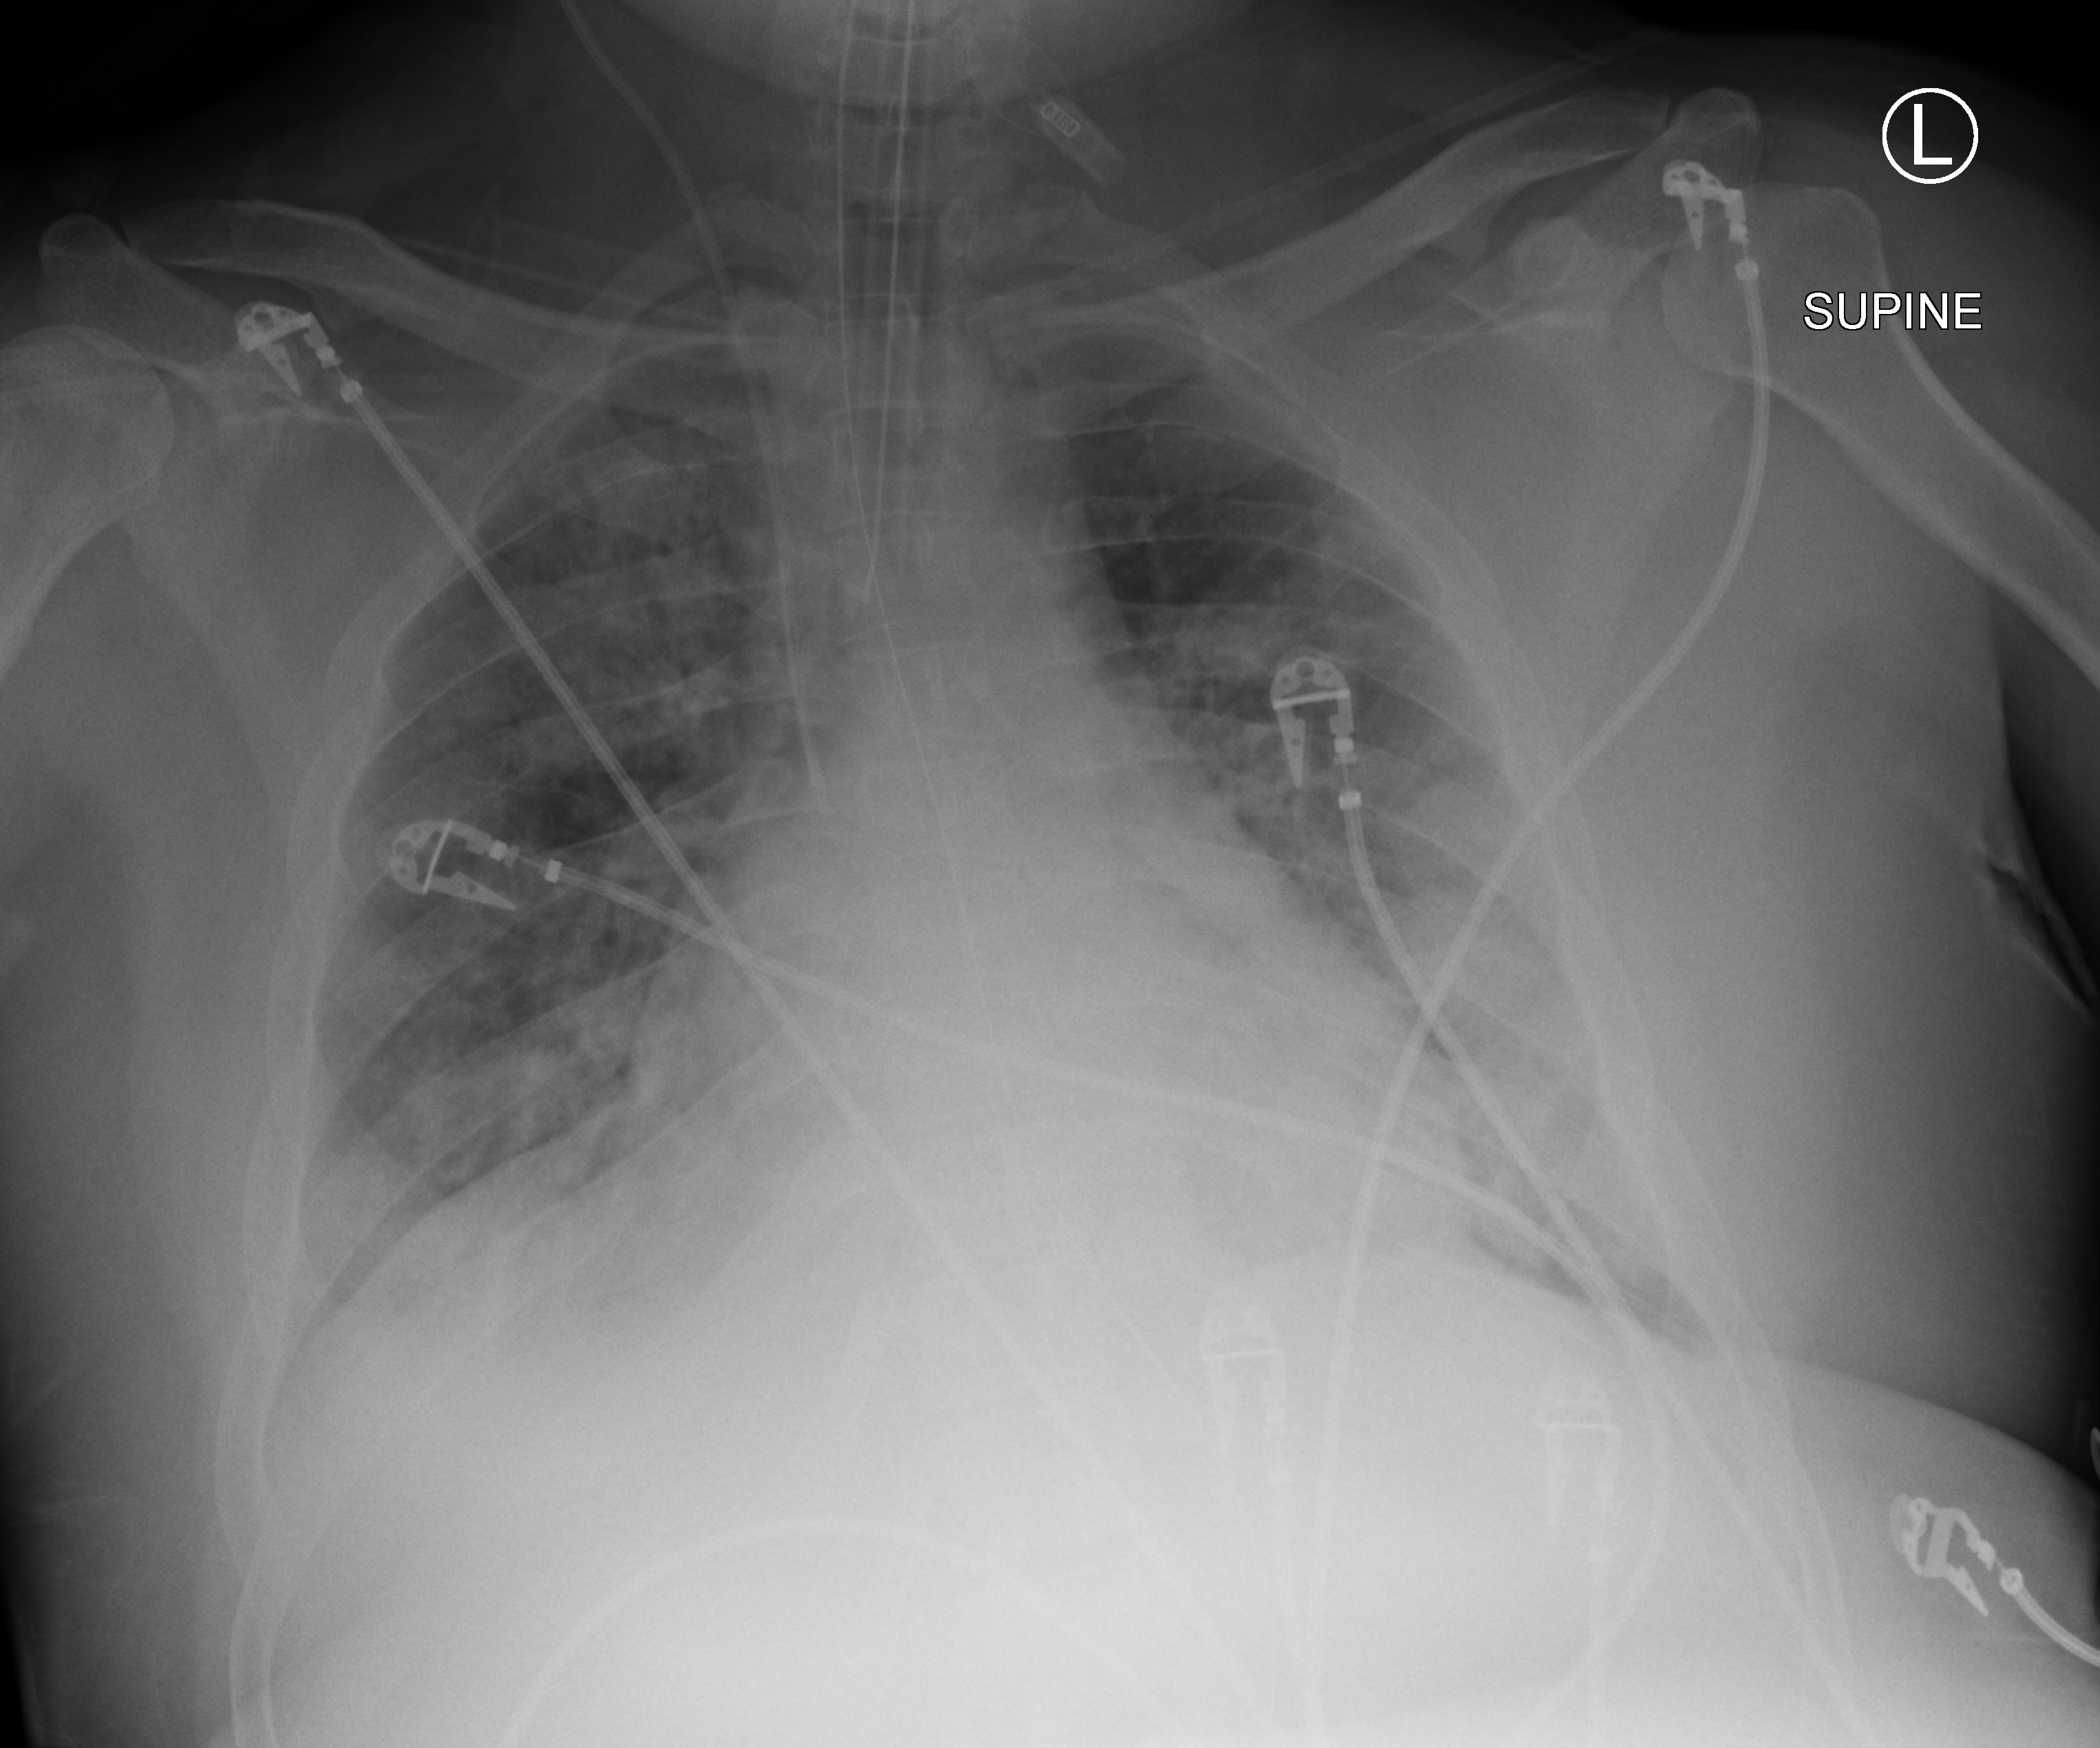
Portable chest radiograph, anteroposterior (AP) projection. Adult patient hospitalised with COVID-19, age 18–59 years.
Hospital-stay facts (about this admission, not read from this image; timing relative to this image not recorded): mechanically ventilated during this hospital stay: yes; COPD (admission record): no.